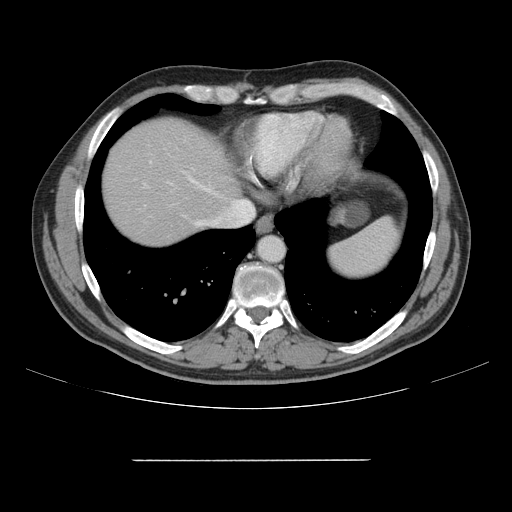
Contrast-enhanced abdominal CT, one axial slice. Slice 138 of 164 in the series (ordered by position). Soft-tissue window (W 400 / L 40 HU). 2.5 mm slice thickness. 512 × 512 image matrix. Male patient, age 54 years. From the clinical record (not read from this slice): diagnosis: colorectal cancer liver metastases, imaged before liver resection; multiple liver metastases: yes; largest metastasis: 1 cm; disease in both lobes: no.
Annotated regions visible in this slice (manually delineated by an expert):
- hepatic veins: bounding box (x1, y1, x2, y2) in pixels: (168, 176, 254, 226)
- liver: (102, 119, 240, 246)
- planned liver remnant (the part of the liver to remain after resection): (103, 119, 239, 246)